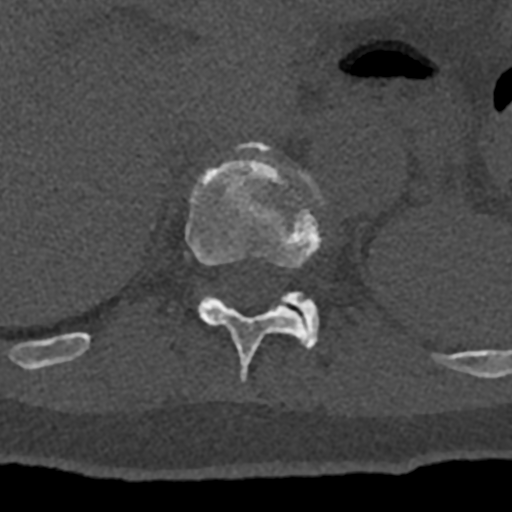
CT including the spine, one axial slice. Position 535 of 797 along the scan axis. 120 kVp. Bone window (W 1800 / L 400 HU). 0.5 mm slice thickness. 512 × 512 image matrix, field of view 160 × 160 mm. Patient: male, 74 years. From the clinical record (not read from this slice): primary cancer: renal; vertebrae with lytic lesions (as recorded): T10, L1, L2, L3, L4, L5.
Structures marked on this image (semi-automatically segmented with operator editing):
- T11 vertebra: box from (x=70, y=141) to (x=324, y=381) px
- T12 vertebra: (x=280, y=291)–(x=319, y=349)